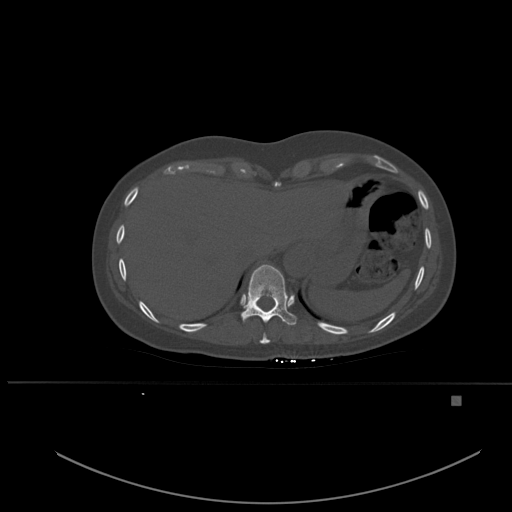
CT including the spine, one axial slice. Slice 291 of 651 in the series (ordered by position). Bone window (W 1800 / L 400 HU). 1.5 mm slice thickness. 512 × 512 image matrix, field of view 443 × 443 mm. Patient: female, 49 years. From the clinical record (not read from this slice): primary cancer: breast.
Outlined on this slice (semi-automatic segmentation, software-assisted and operator-edited):
- T10 vertebra: bounding box (x1, y1, x2, y2) in pixels: (241, 264, 297, 325)
- T9 vertebra: (260, 333, 270, 344)